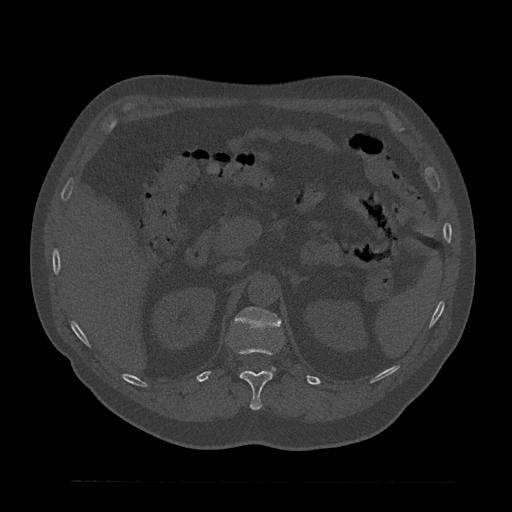
CT including the spine, one axial slice. Position 207 of 797 along the scan axis. Reconstruction kernel Br40s/3. 120 kVp. Bone window (W 1800 / L 400 HU). 0.5 mm slice thickness. 512 × 512 image matrix, field of view 430 × 430 mm. Male patient, age 61 years. From the clinical record (not read from this slice): primary cancer: prostate.
Annotated regions visible in this slice (semi-automatically segmented with operator editing):
- L1 vertebra: bounding box [x1, y1, x2, y2] px = [235, 307, 281, 371]
- T12 vertebra: [237, 346, 274, 410]